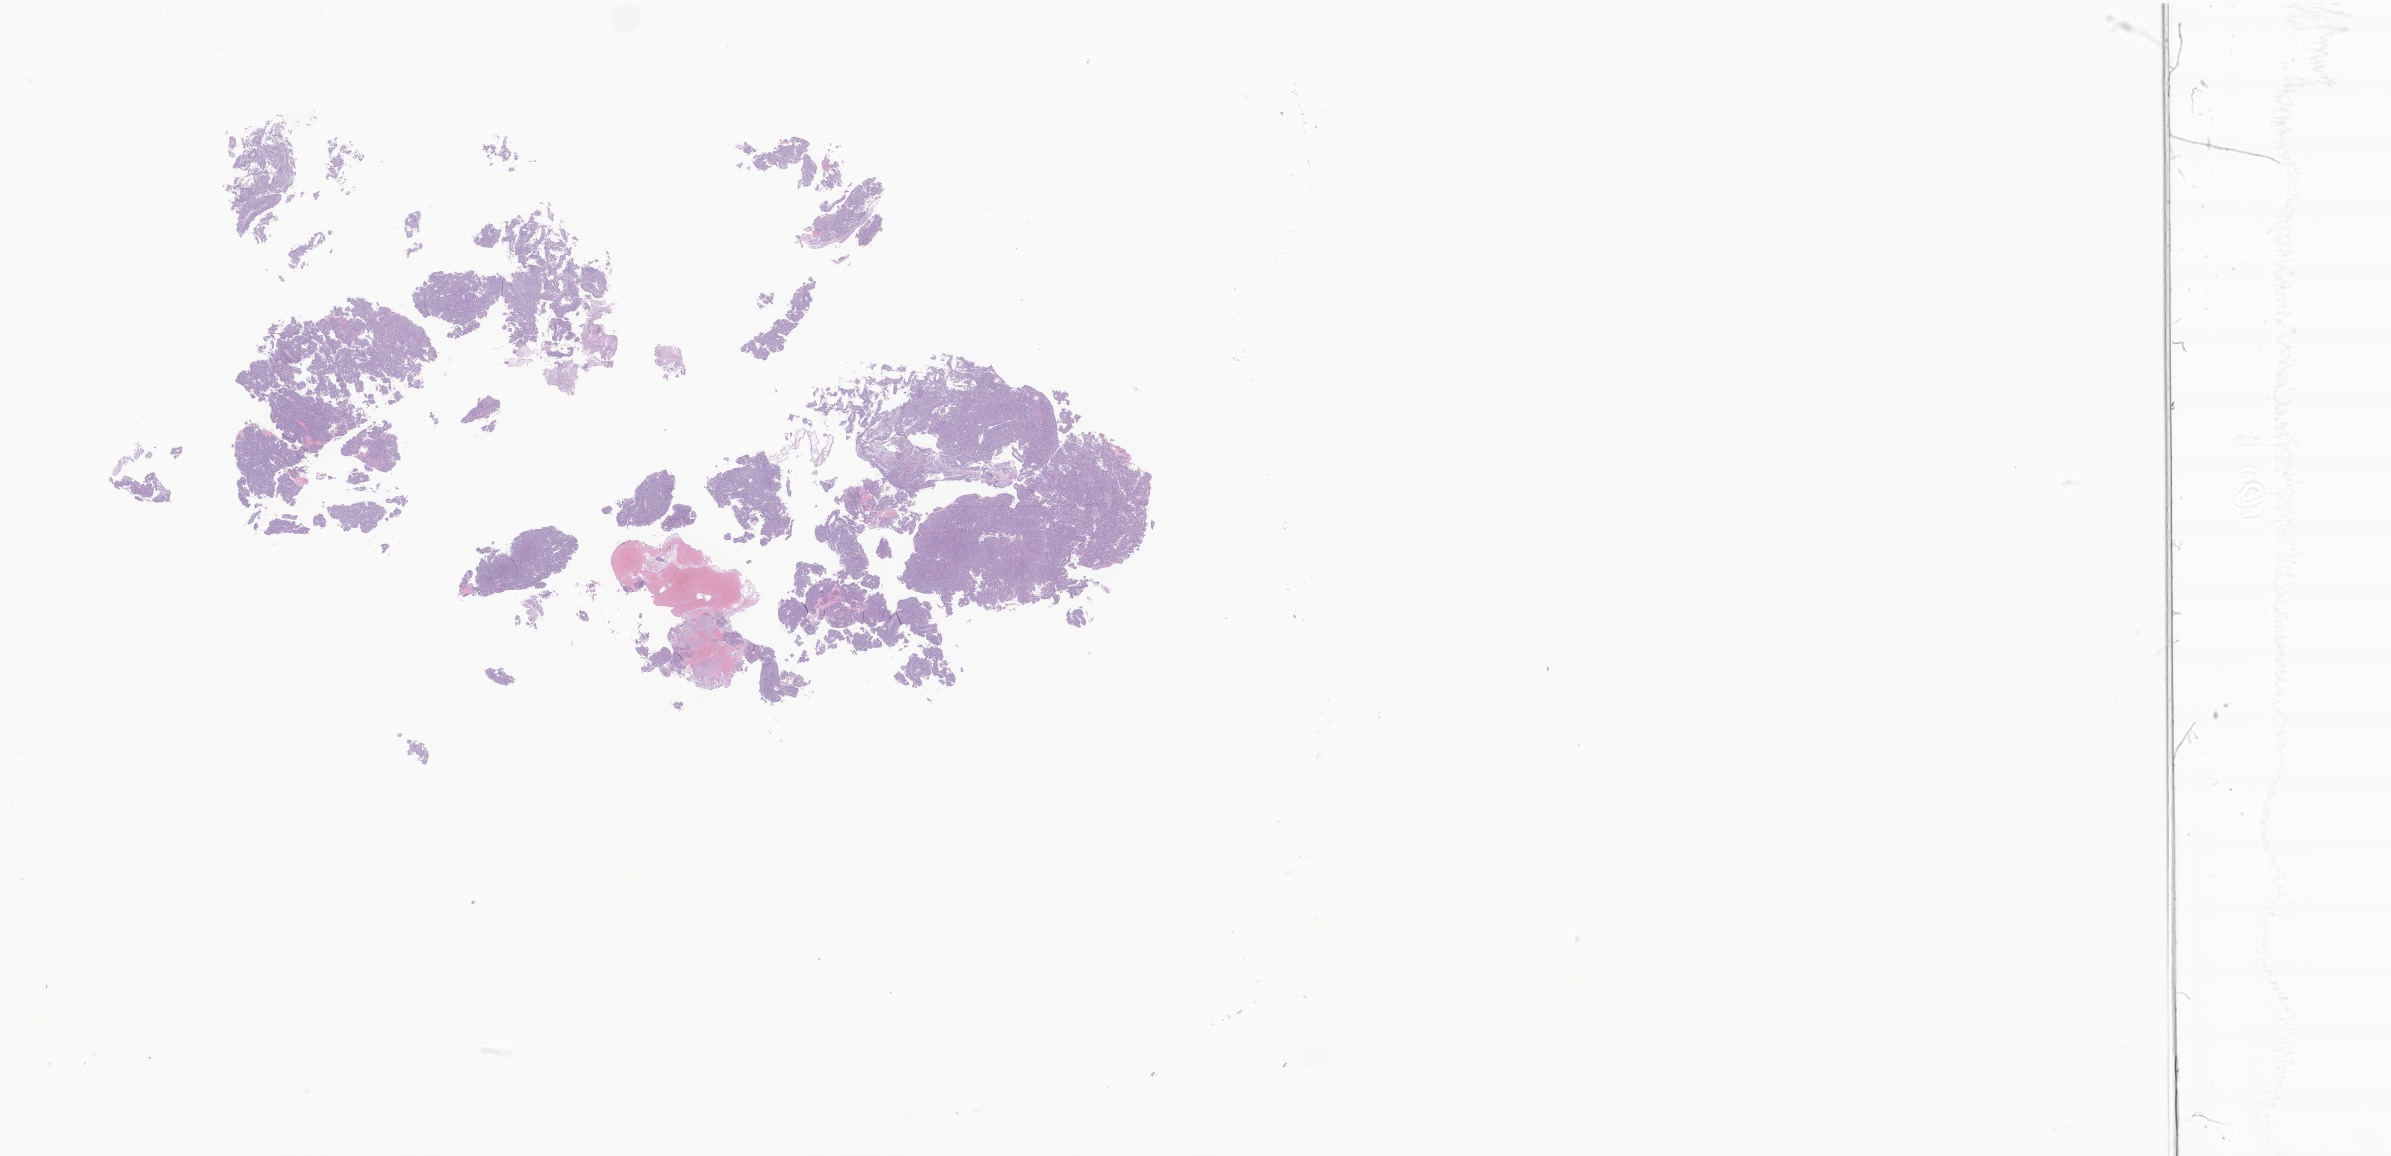
Whole-slide image, H&E stain of tumor tissue from the brain — shown as a low-resolution overview of the whole scanned area (about 40.3 x 19.5 mm); formalin-fixed, paraffin-embedded (FFPE) tissue. Male patient, age 403 days.
* diagnosis (ICD-O-3 morphology term): Glioma, malignant